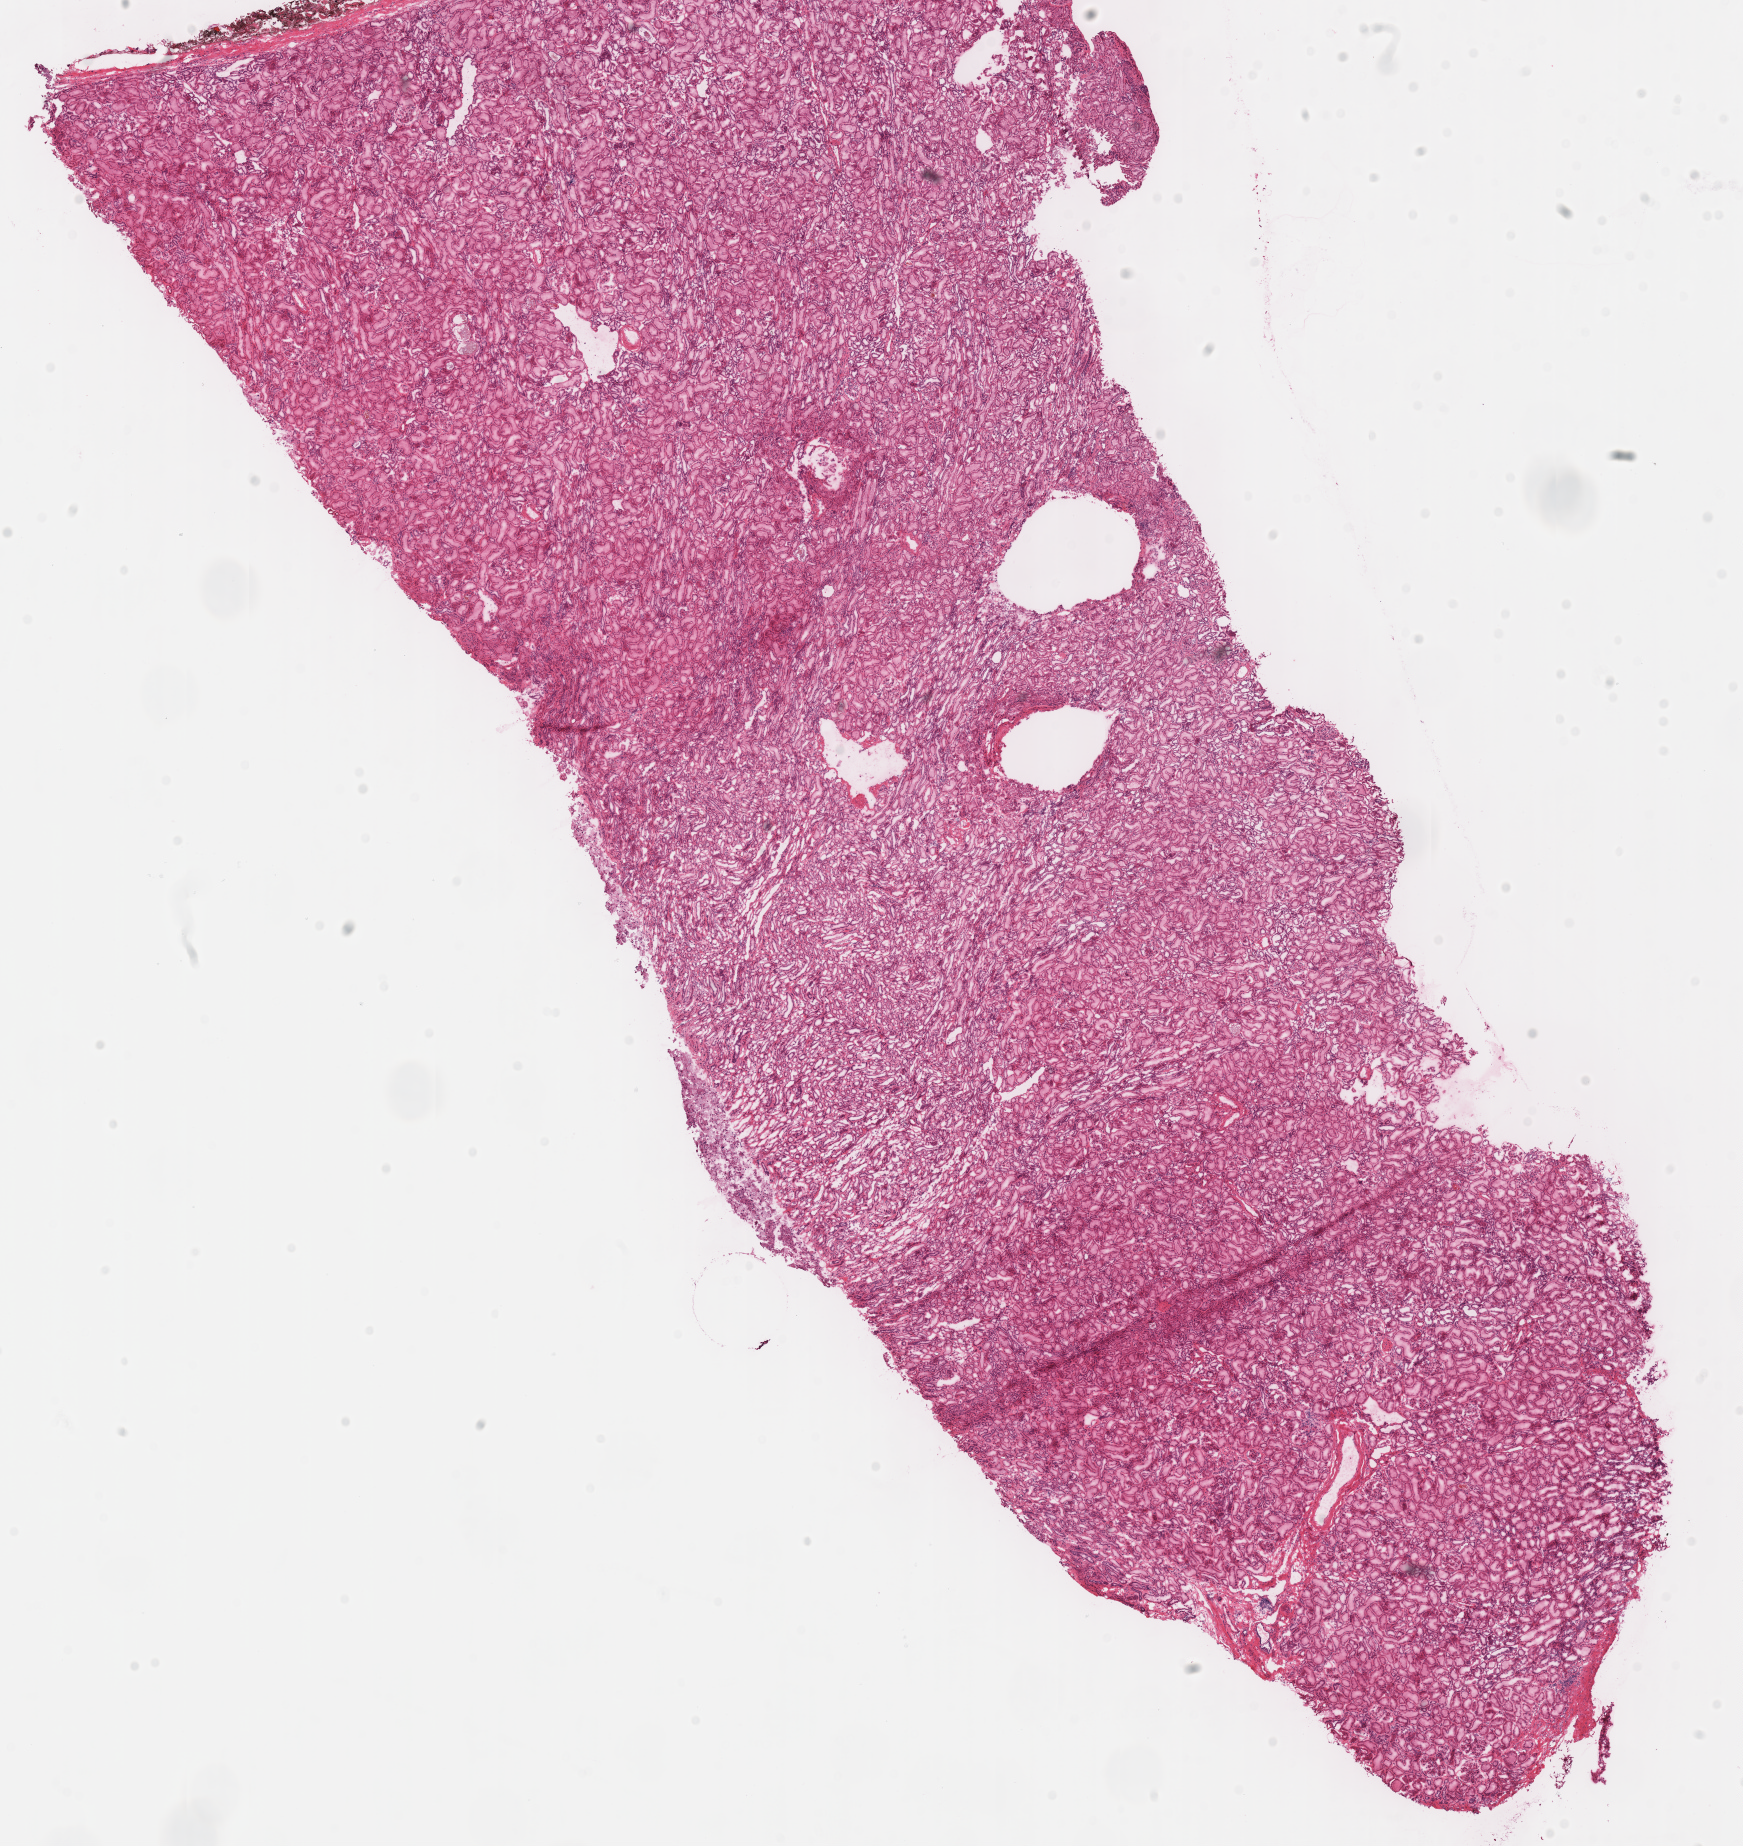
Hematoxylin and eosin (H&E) stained whole-slide image — a low-resolution overview of the entire scanned area, about 13.7 x 14.5 mm; frozen section; sample: solid tissue normal (non-tumour tissue), kidney. Female, age 48 years at initial diagnosis. Infiltration values recorded for this section: lymphocyte infiltration 1%, monocyte infiltration 0%, neutrophil infiltration 0%.
- this section: solid tissue normal (non-tumour) sample from the same patient
- patient diagnosis: Renal cell carcinoma, chromophobe type